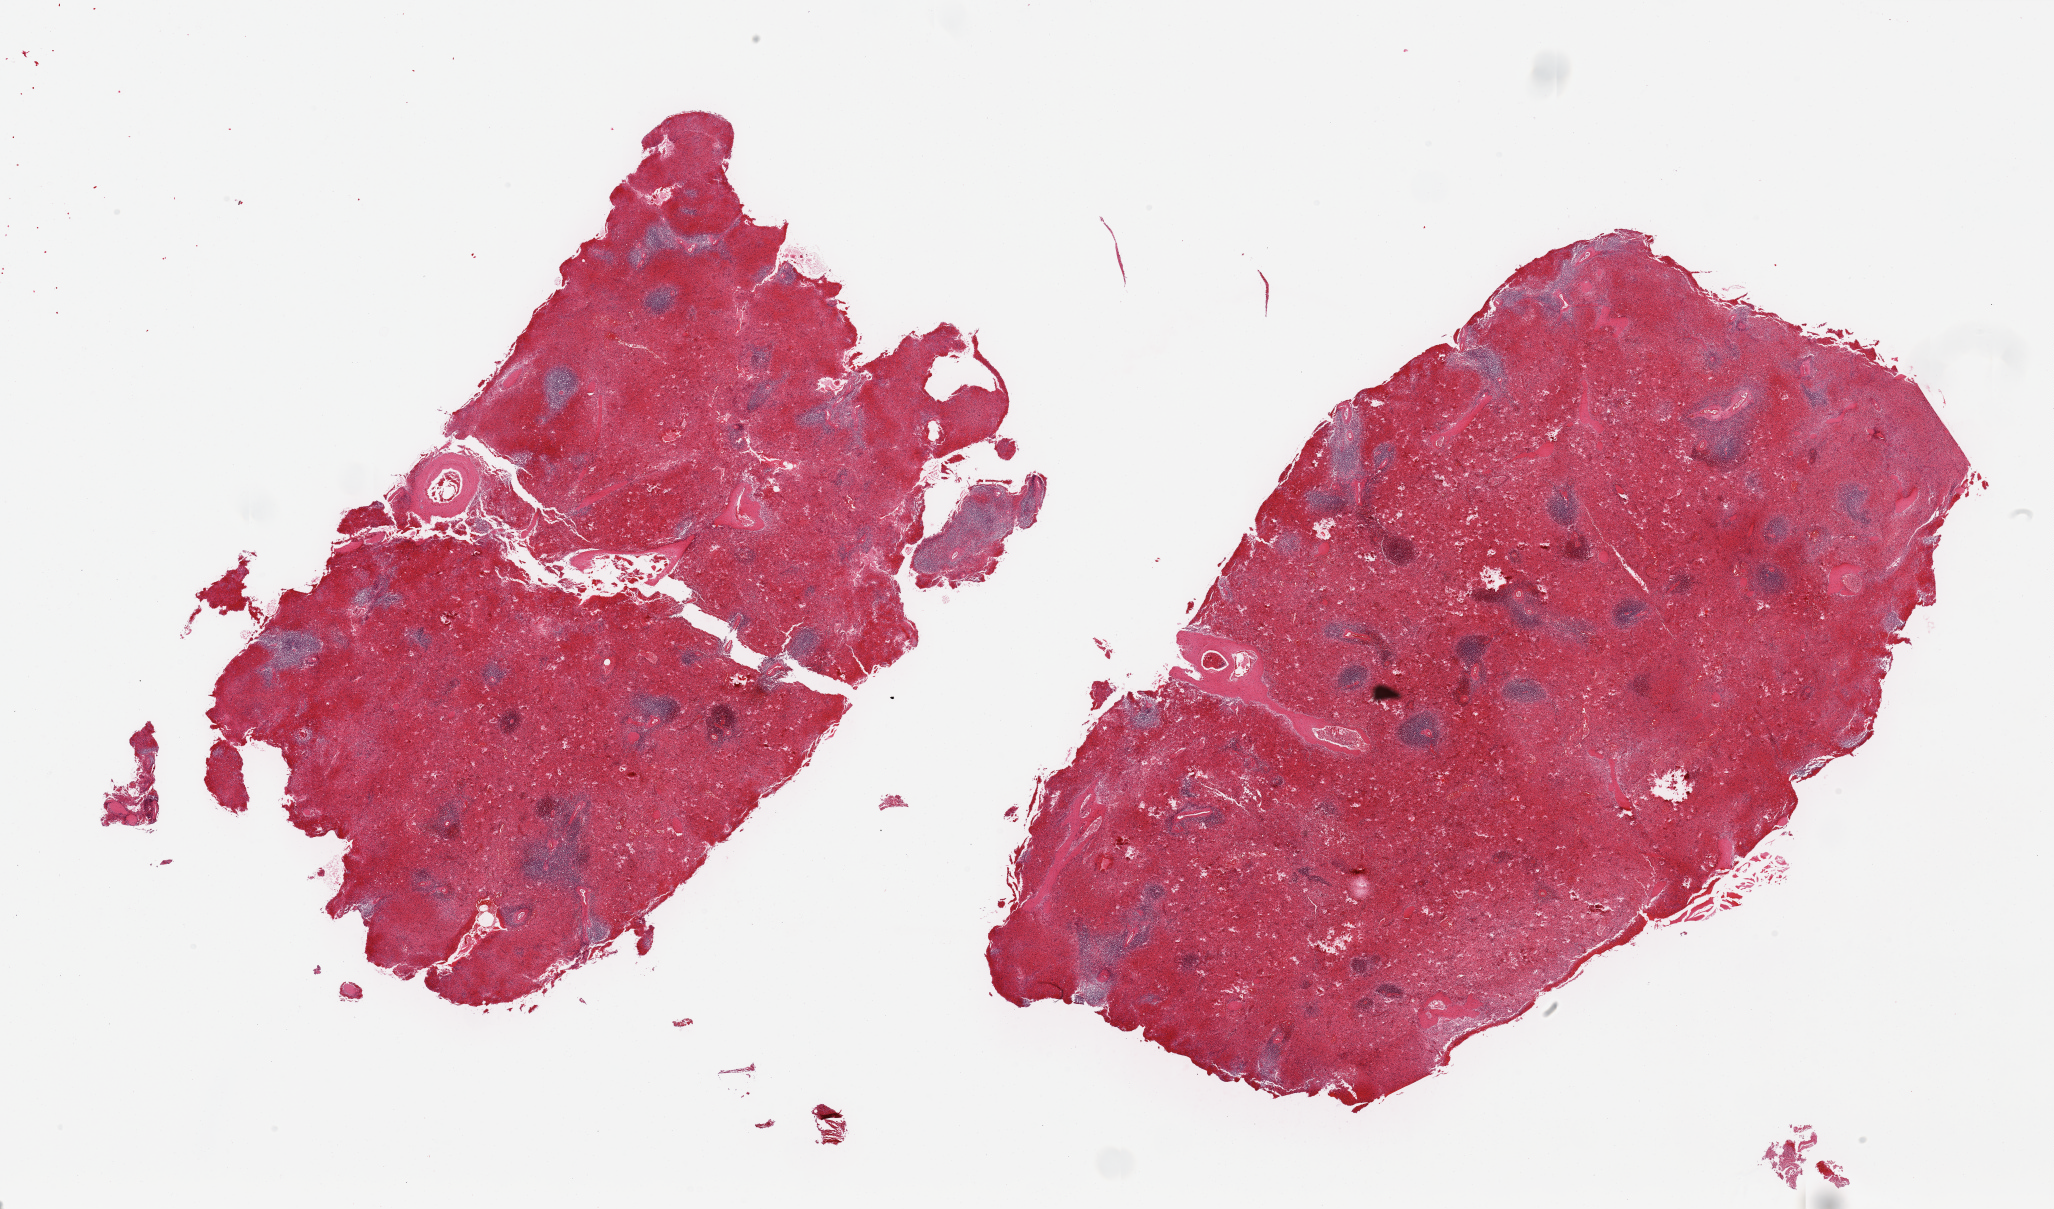
H&E whole-slide image, brightfield — whole scanned area (about 32.5 x 19.1 mm) shown as a low-resolution overview, PAXgene-fixed, paraffin-embedded tissue, target tissue: spleen, tissue donor sample. Donor: male.
Review note (as recorded): 2 pieces; moderately congested.